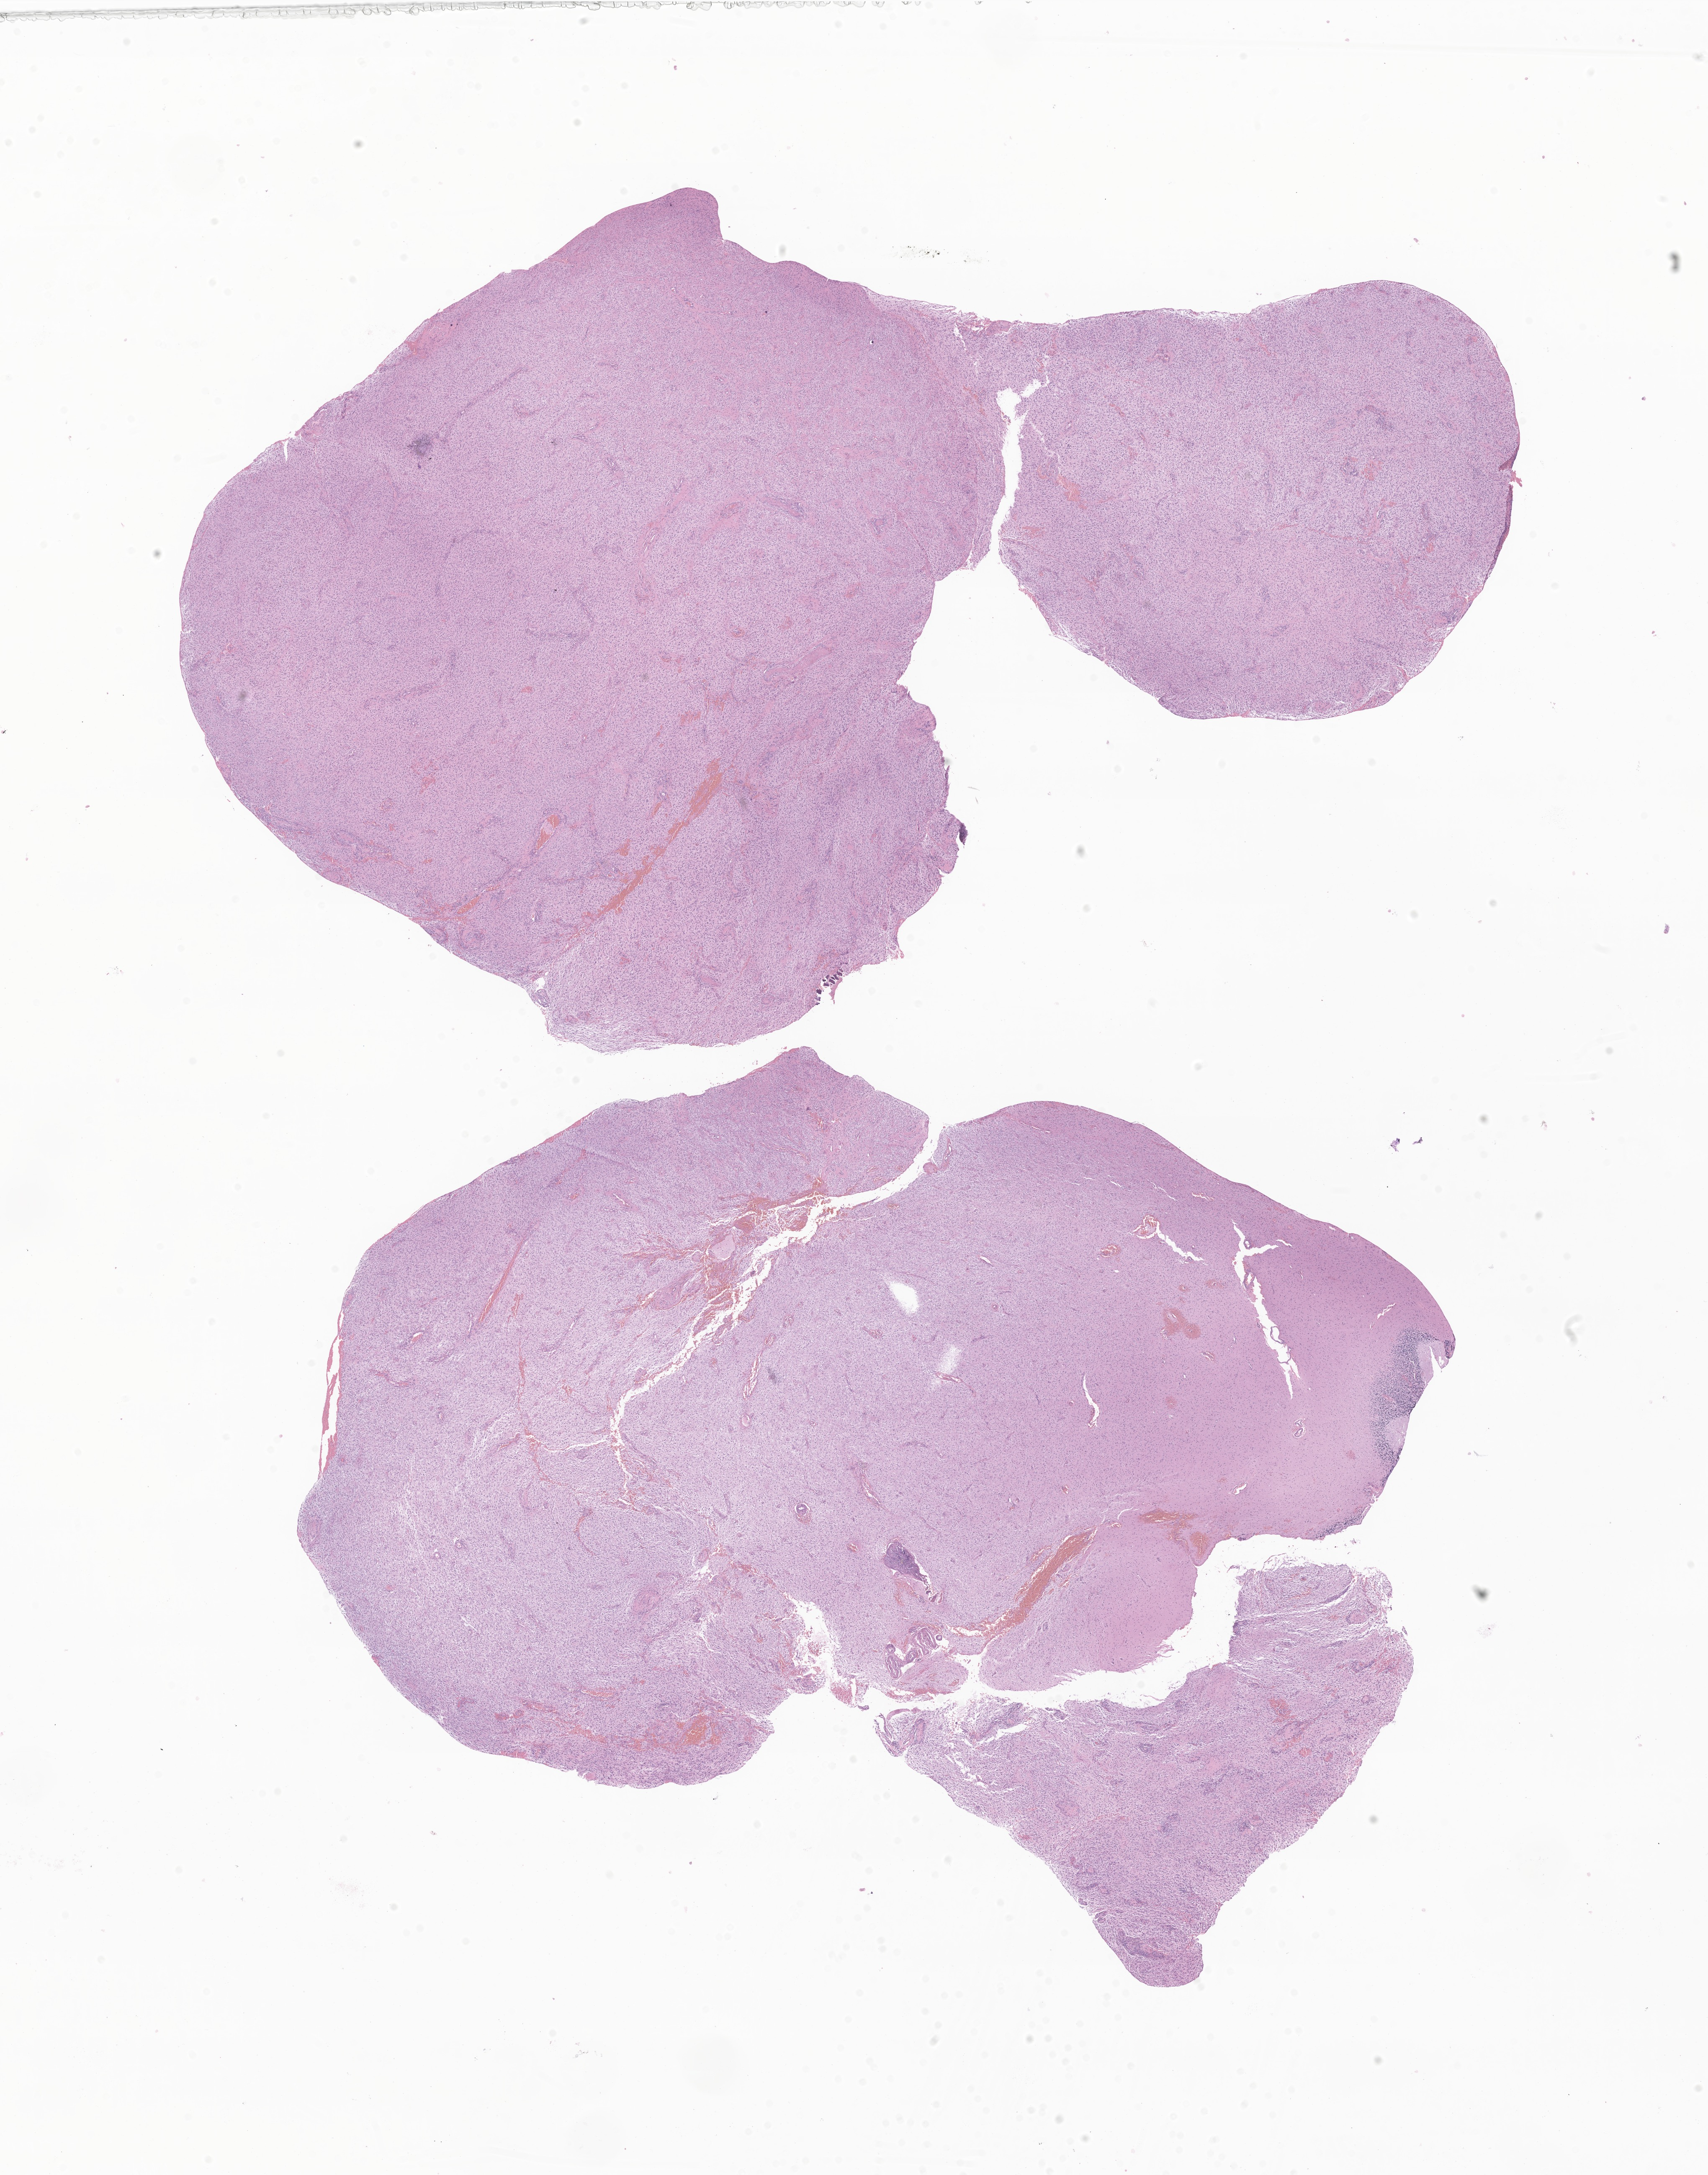
Hematoxylin and eosin (H&E) whole-slide image of tumor tissue from the brain, a low-resolution overview of the entire scanned area, about 17.2 x 21.9 mm. Formalin-fixed paraffin-embedded section. Patient female; age 146 months (12 years 2 months).
- diagnosis: Pilocytic astrocytoma